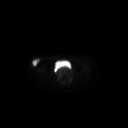
FDG PET of an extremity soft-tissue mass (from a PET/CT study), one axial slice. 128 × 128 image matrix, field of view 700 × 700 mm. Patient: female, 34 years. From the clinical record (not read from this slice): histological type: synovial sarcoma; grade: intermediate; site of the primary tumour: right thigh.
Annotated regions visible in this slice (expert contour drawn on MRI and transferred to this co-registered scan by the dataset authors):
- gross tumour volume including surrounding oedema: bounding box <31,58,40,67> (left, top, right, bottom; pixels)
- gross tumour volume (mass): <31,58,40,67>